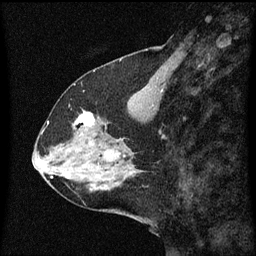
Breast MRI (dynamic contrast-enhanced), one sagittal slice; position 25 of 60 along the scan axis; dynamic contrast-enhanced series, image 2 of 3 at this slice position (ordered by acquisition); 1.5 T; TE 4.2 ms, TR 8.4 ms; 256 × 256 image matrix, field of view 200 × 200 mm. Patient: female, 59 years.
Outlined on this slice (semi-automatic segmentation, software-assisted and operator-edited):
- analysis volume of interest (the breast-tissue region the enhancement analysis was run in; not a lesion): box from (x=73, y=112) to (x=99, y=137) px
- tumour enhancement mask (voxels above the 70 % enhancement threshold inside the analysis volume of interest): (x=76, y=112)–(x=96, y=127)